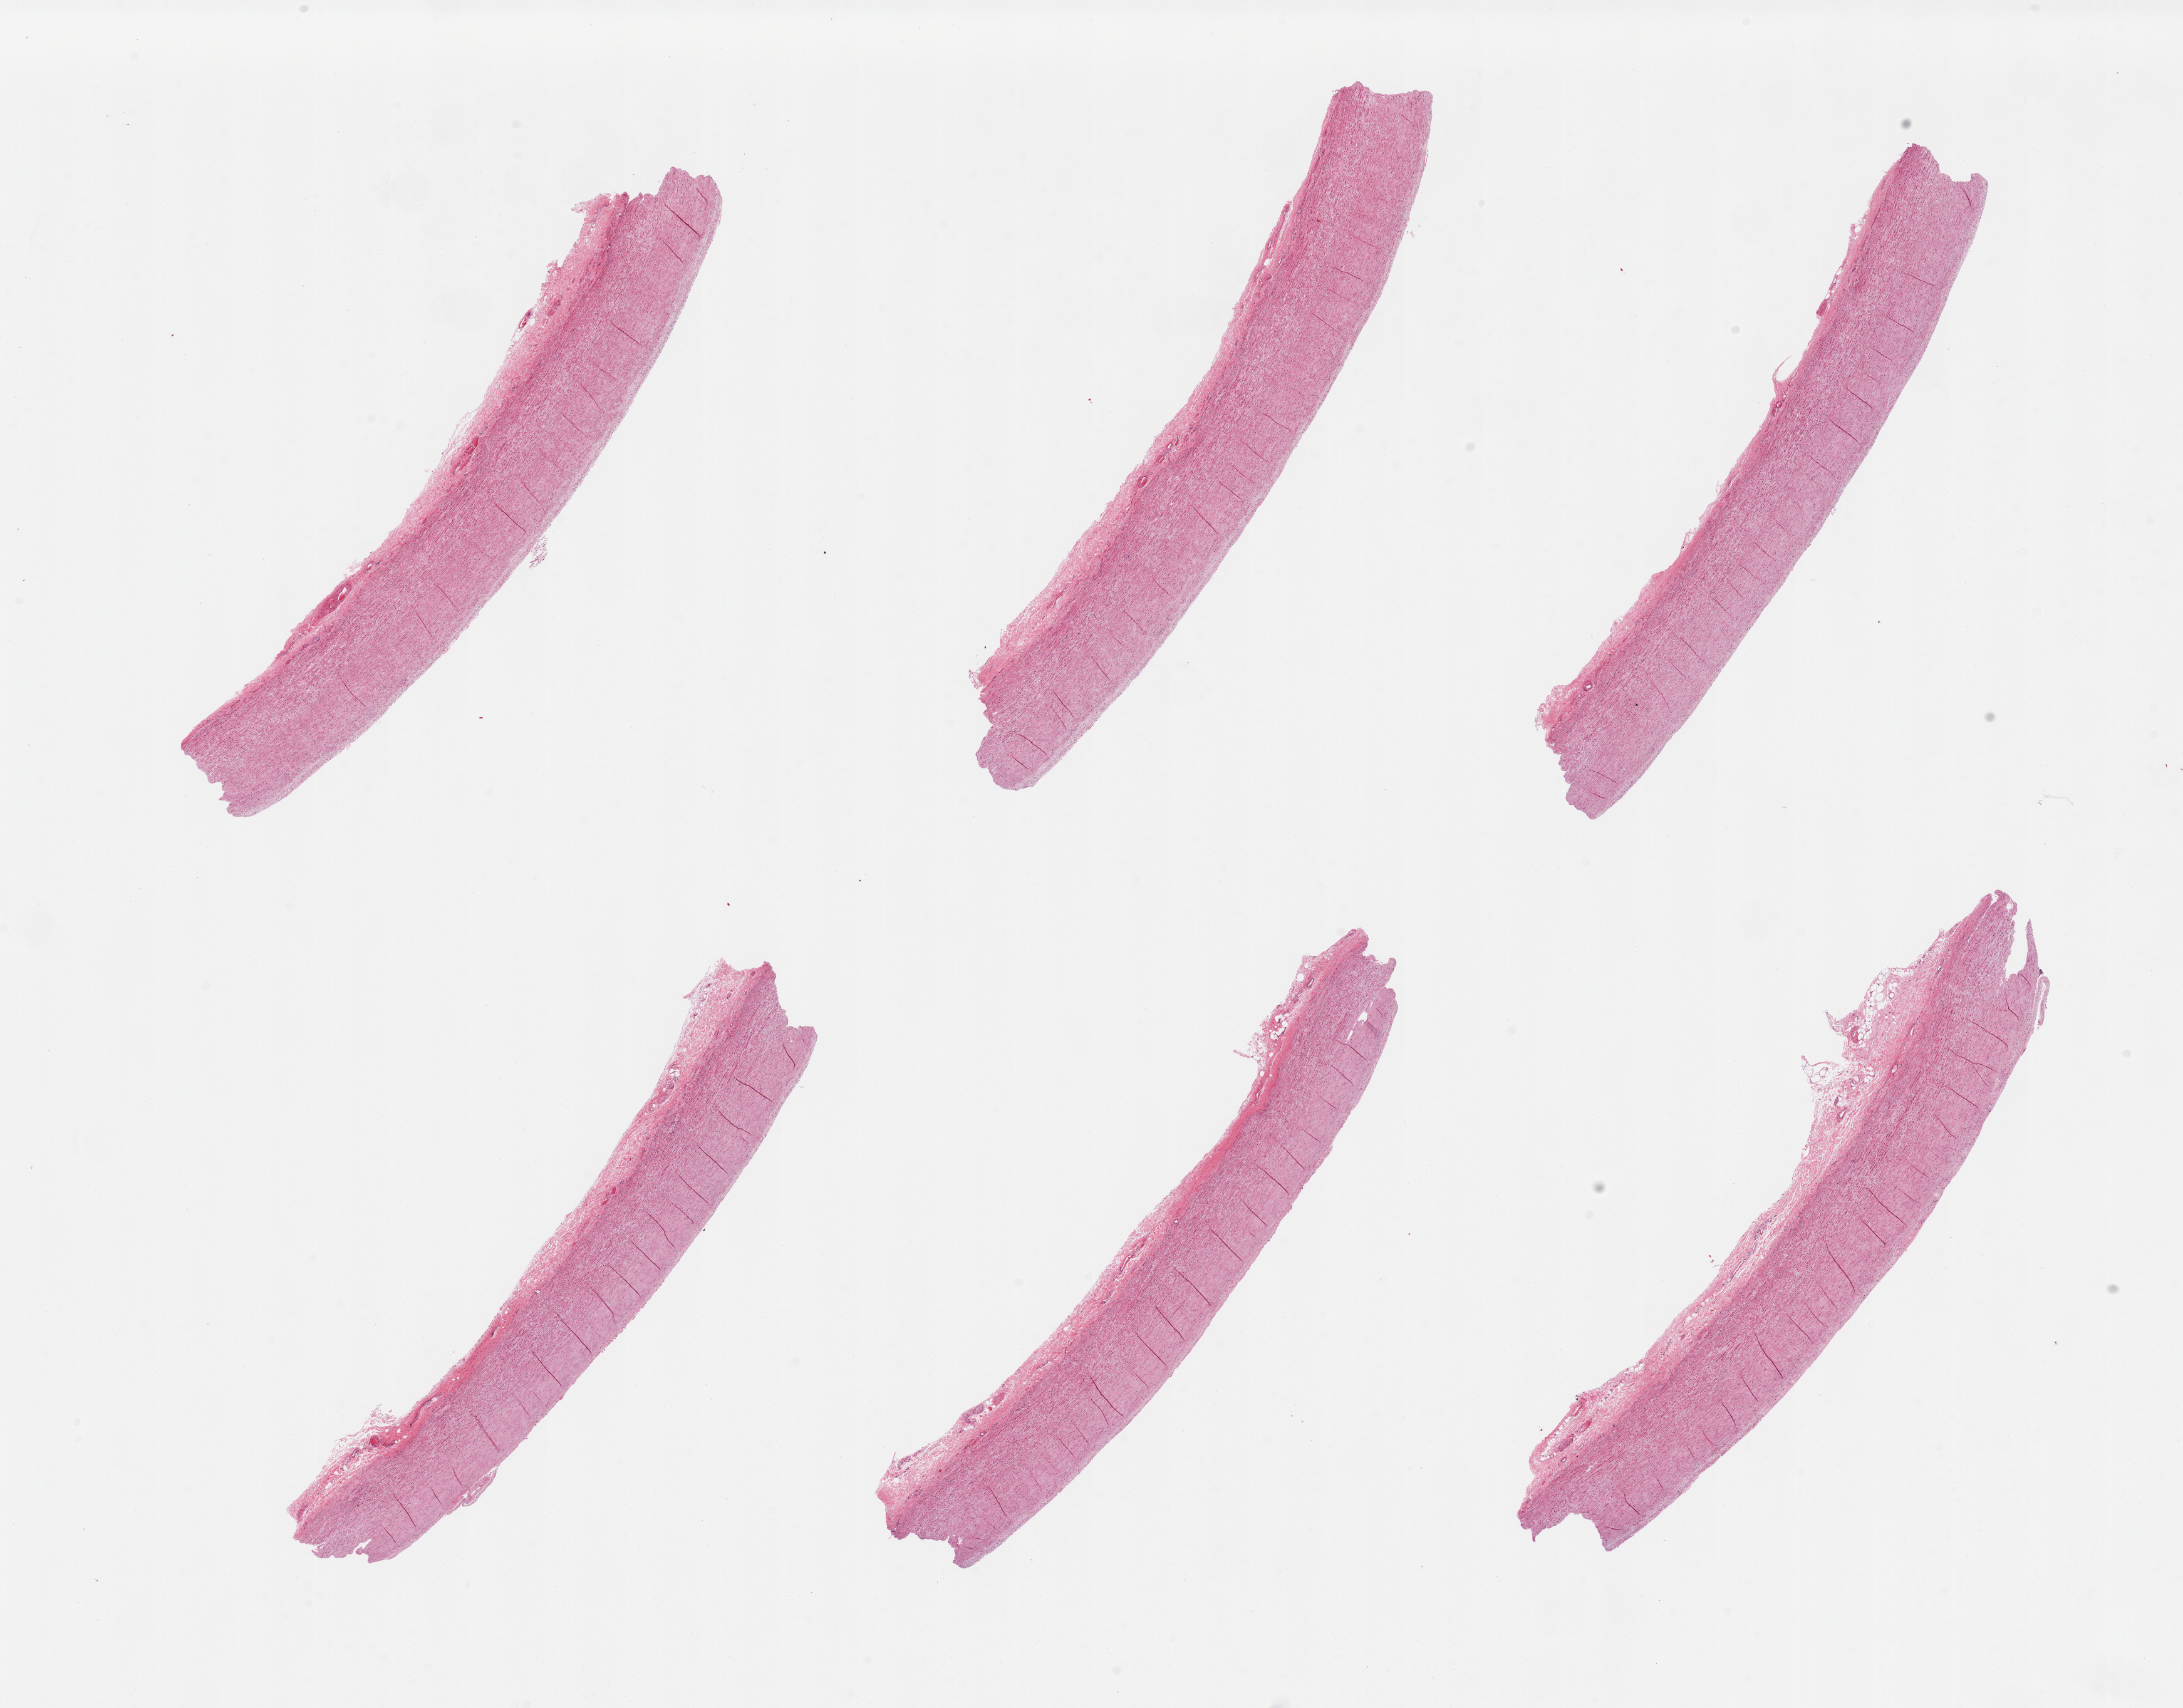
Whole-slide image, H&E stain, low-resolution overview of the scanned area, about 27.6 x 21.6 mm (slide scanned at 20x), PAXgene-fixed paraffin-embedded (PFPE) section, section of aorta (target tissue), tissue donor sample. Male donor.
• review note (as recorded): 6 pieces